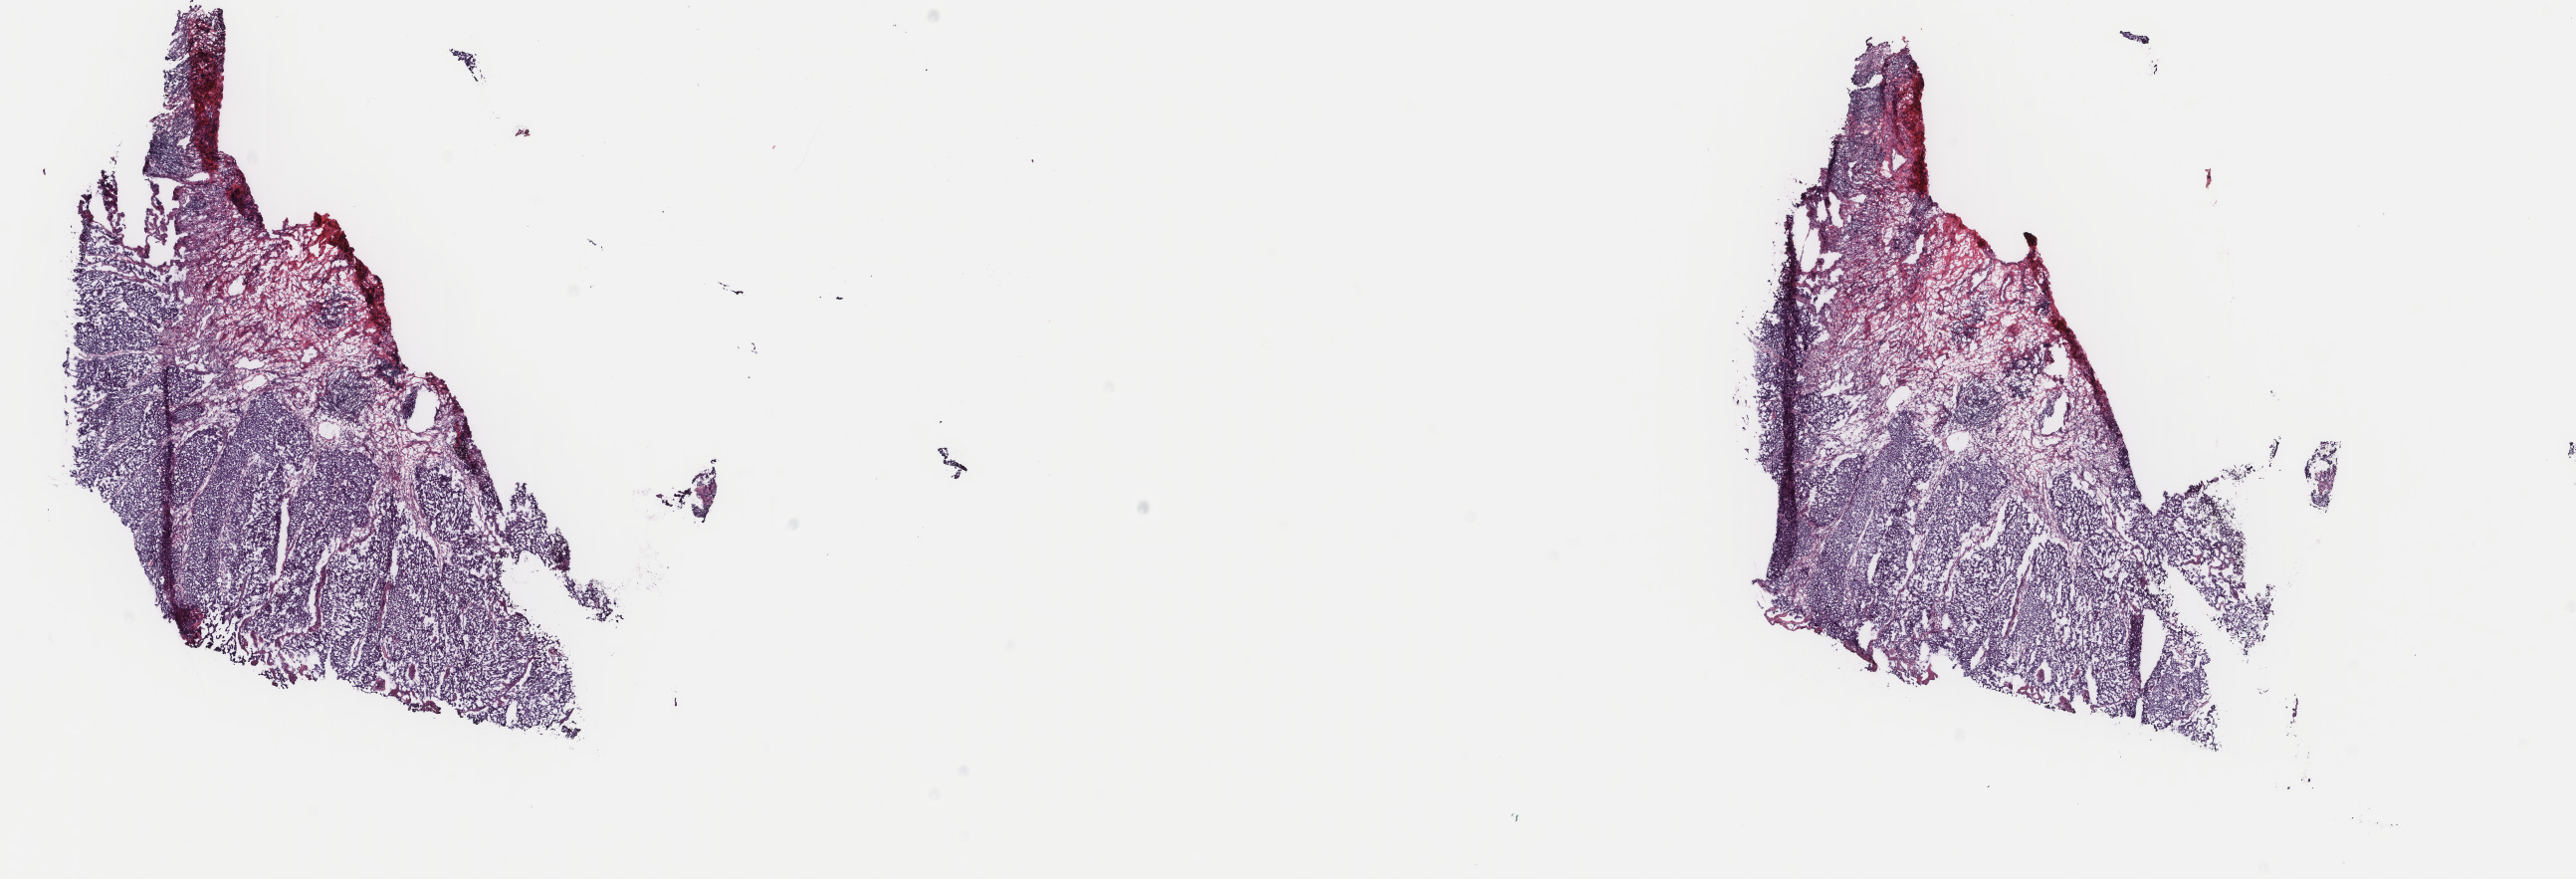
Digitized H&E tissue section (whole slide), low-resolution overview of the scanned area, about 20.5 x 7.0 mm; frozen section; sample: primary tumour, bladder. Male patient; age at initial diagnosis 72 years. Histologic grade: high grade. Pathologist review of this section (percent, as recorded): tumour cells 75%, tumour nuclei 75%, normal cells 0%, stromal cells 25%, necrosis 0%. Infiltration values recorded for this section: lymphocyte infiltration 6%, monocyte infiltration 2%, neutrophil infiltration 2%.
- lymph nodes positive (case pathology): 1 of 14 examined
- histologic diagnosis: Transitional cell carcinoma
- AJCC pathologic stage: IV (7th edition)